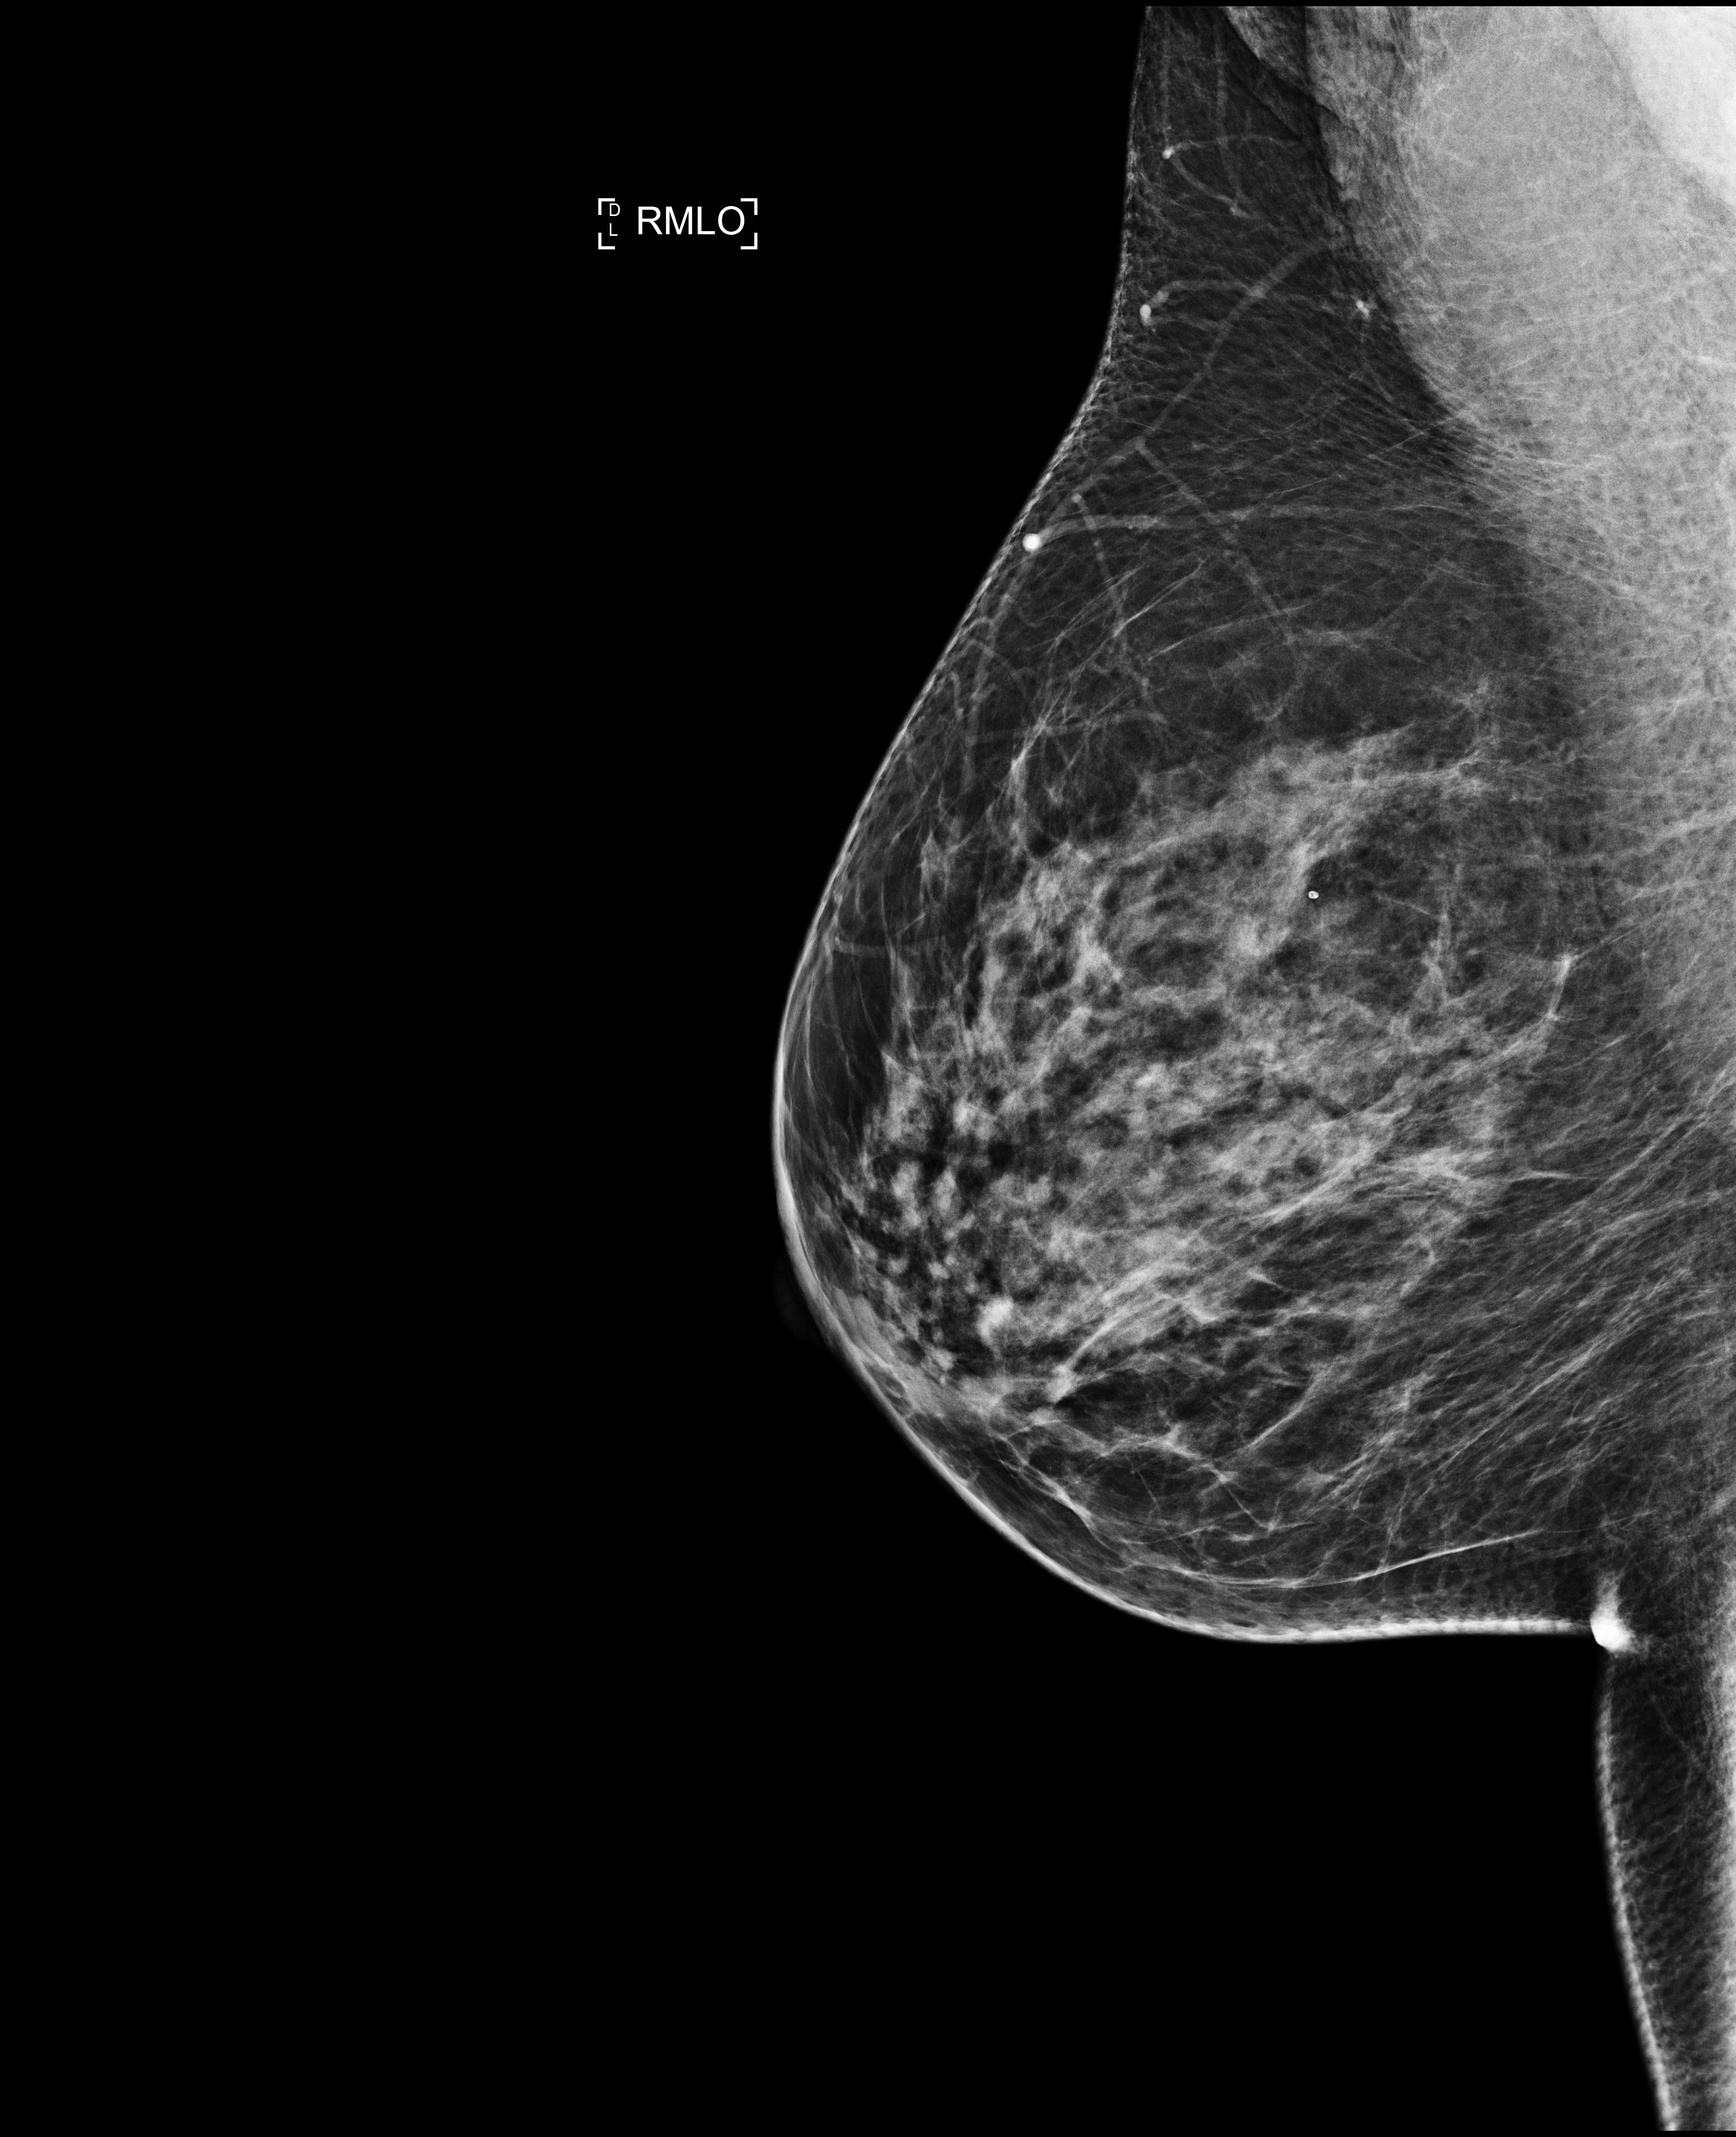
Annual screening mammography examination. Patient aged 47 years (female).
Image type: full-field digital mammogram. Breast: right. Projection: mediolateral oblique (MLO) view.